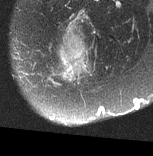
MRI of an extremity soft-tissue mass, one axial slice; slice 20 of 77 in the series (ordered by position); T2-weighted fat-saturated; MR volume resampled by the dataset authors to the PET/CT grid (not the native acquisition matrix); 153 × 156 image matrix, field of view 149 × 152 mm. Female patient. From the clinical record (not read from this slice): histological type: synovial sarcoma; grade: intermediate; site of the primary tumour: right buttock.
Structures marked on this image (expert contour drawn on MRI and transferred to this co-registered scan by the dataset authors):
- gross tumour volume including surrounding oedema: box from (x=55, y=22) to (x=90, y=80) px
- gross tumour volume (mass): (x=55, y=36)–(x=86, y=80)